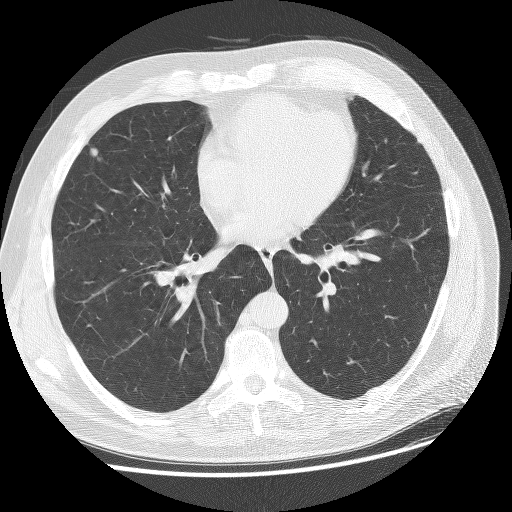
Low-dose screening chest CT, one axial slice. 120 kVp. Lung window (W 1500 / L -600 HU). 2.5 mm slice thickness. 512 × 512 image matrix, field of view 380 × 380 mm.
Outlined on this slice (expert manual segmentation):
- lesion 3 (tumor, upper lobe of right lung): bounding box (x1, y1, x2, y2) in pixels: (91, 148, 98, 156)